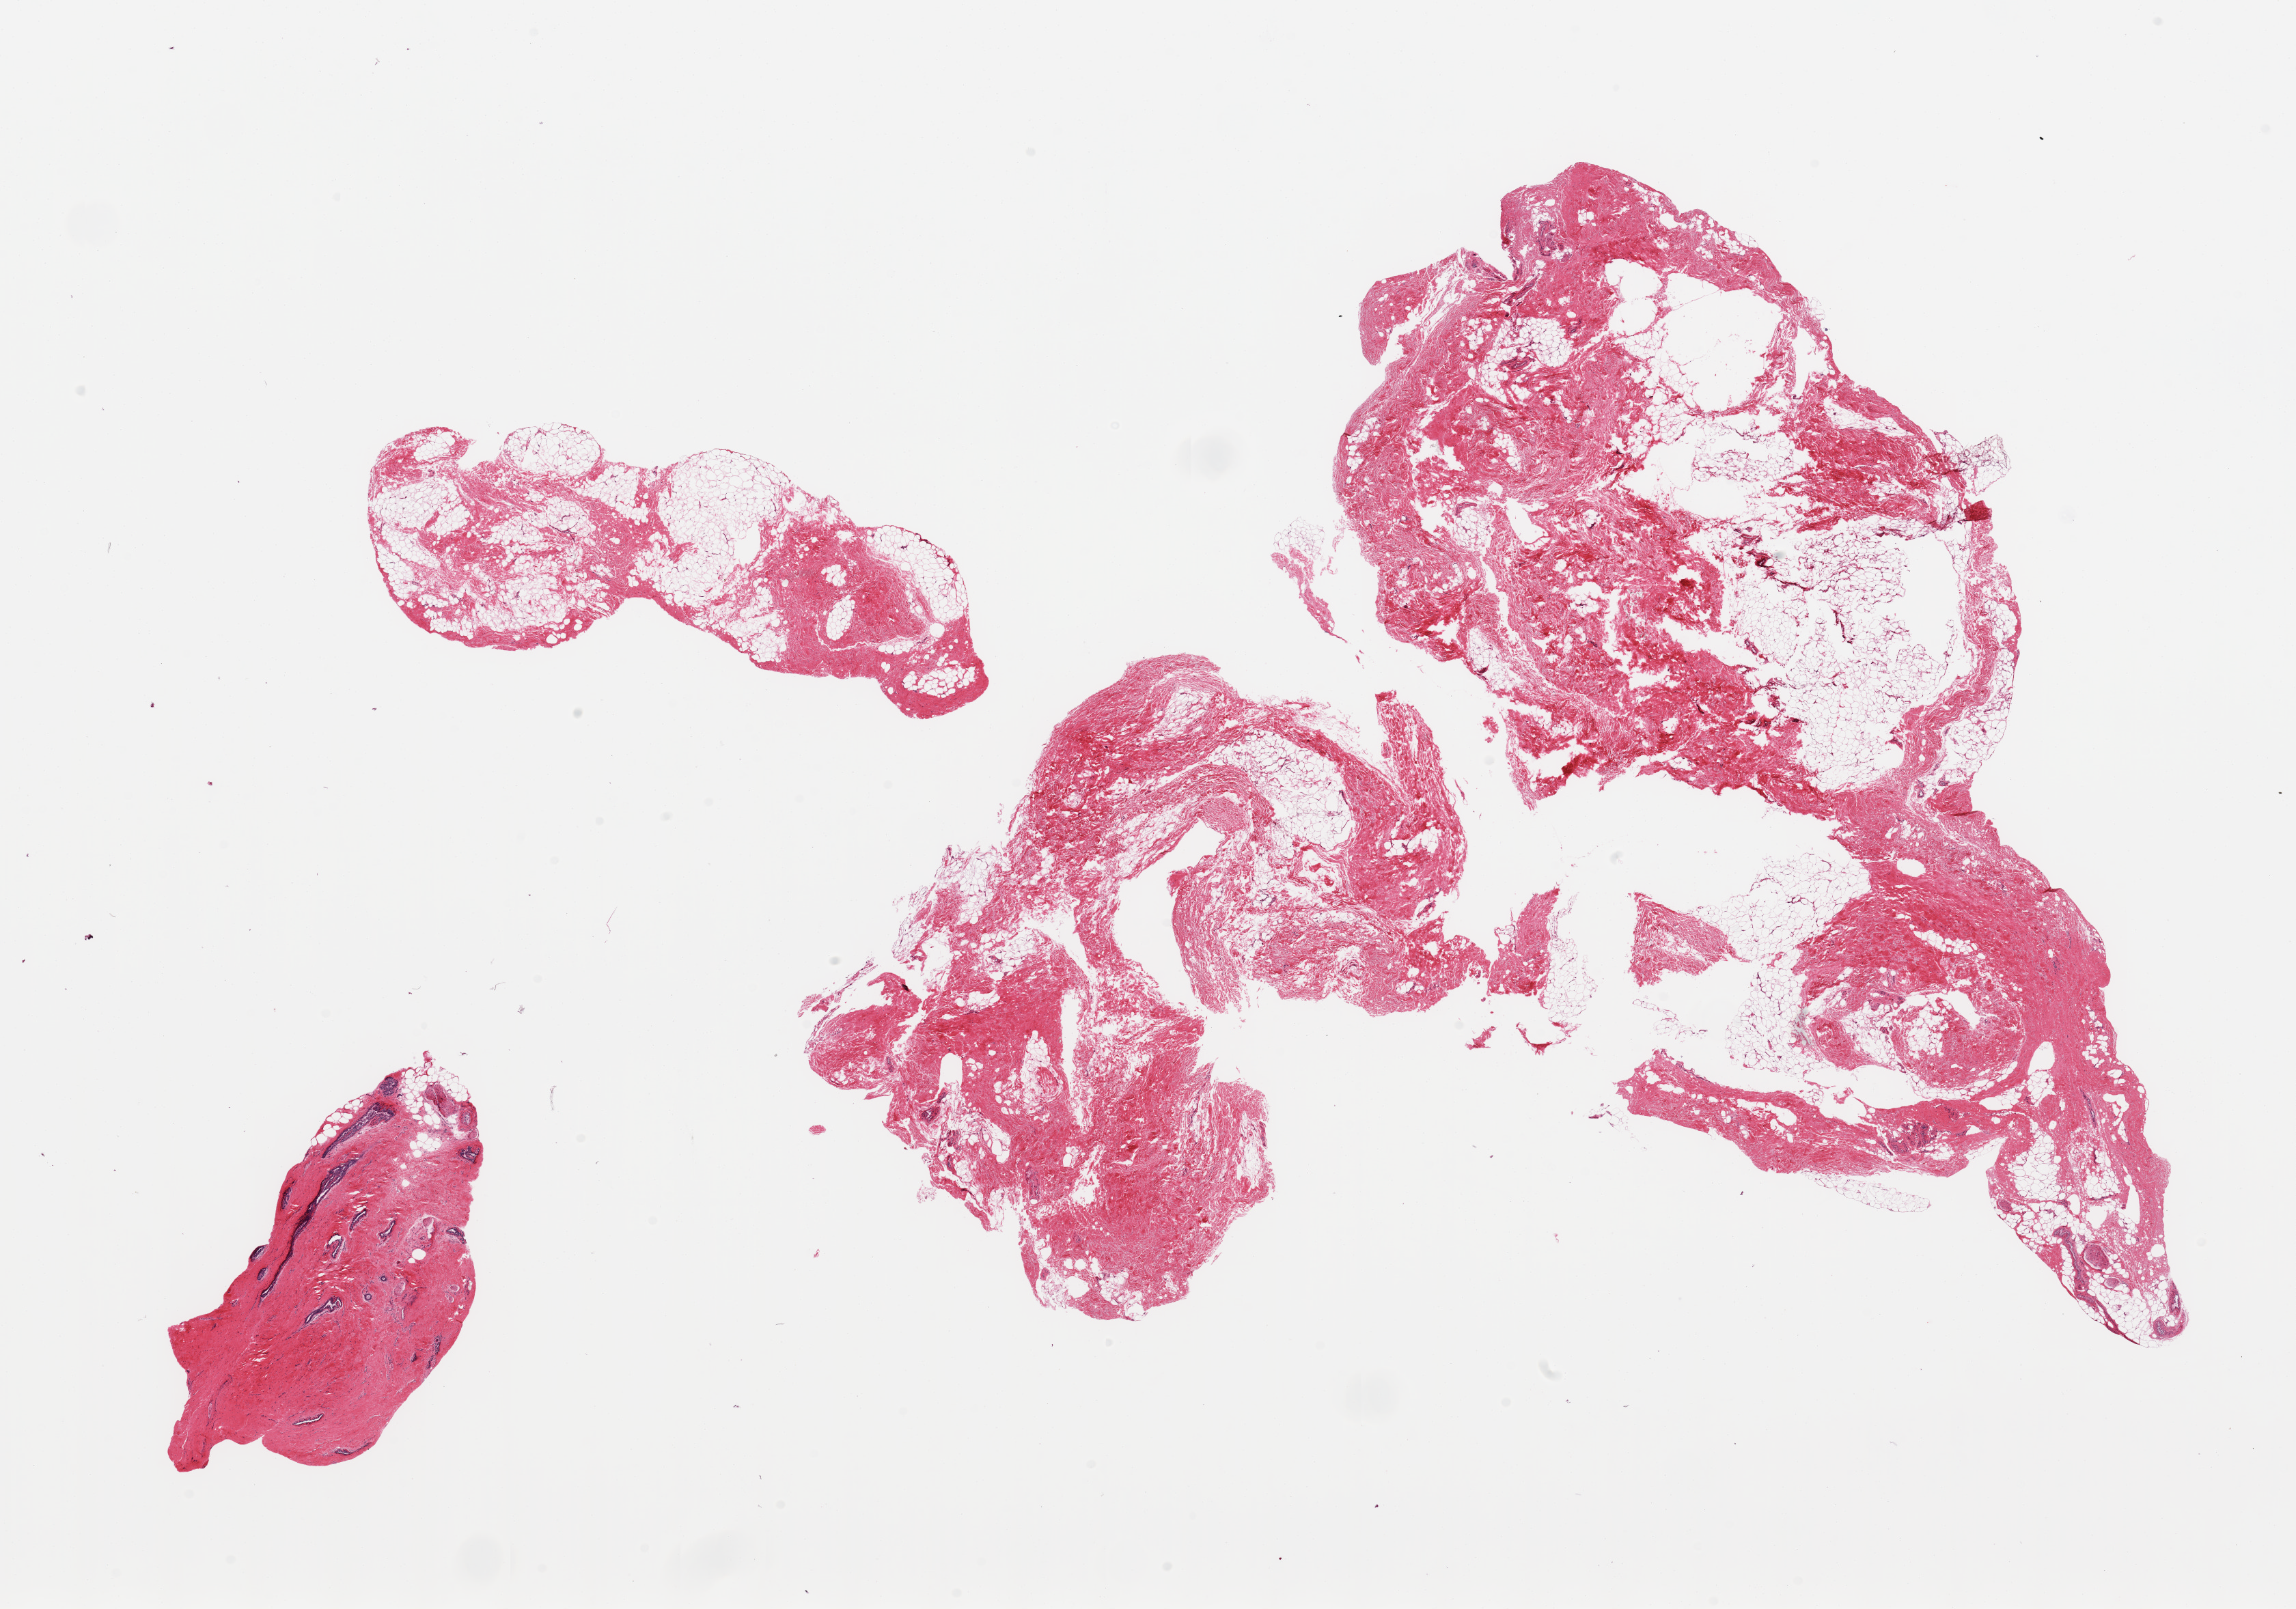
Whole-slide image, hematoxylin and eosin (H&E) stain, a low-resolution overview of the entire scanned area, about 26.6 x 18.6 mm, PAXgene-fixed, paraffin-embedded tissue, target tissue: breast, tissue donor sample. Donor: male.
- review note (as recorded): 4 pieces, mainly fibroadipose elements; one piece with stromal and ductal gynecomastoid hyperplasia, piece